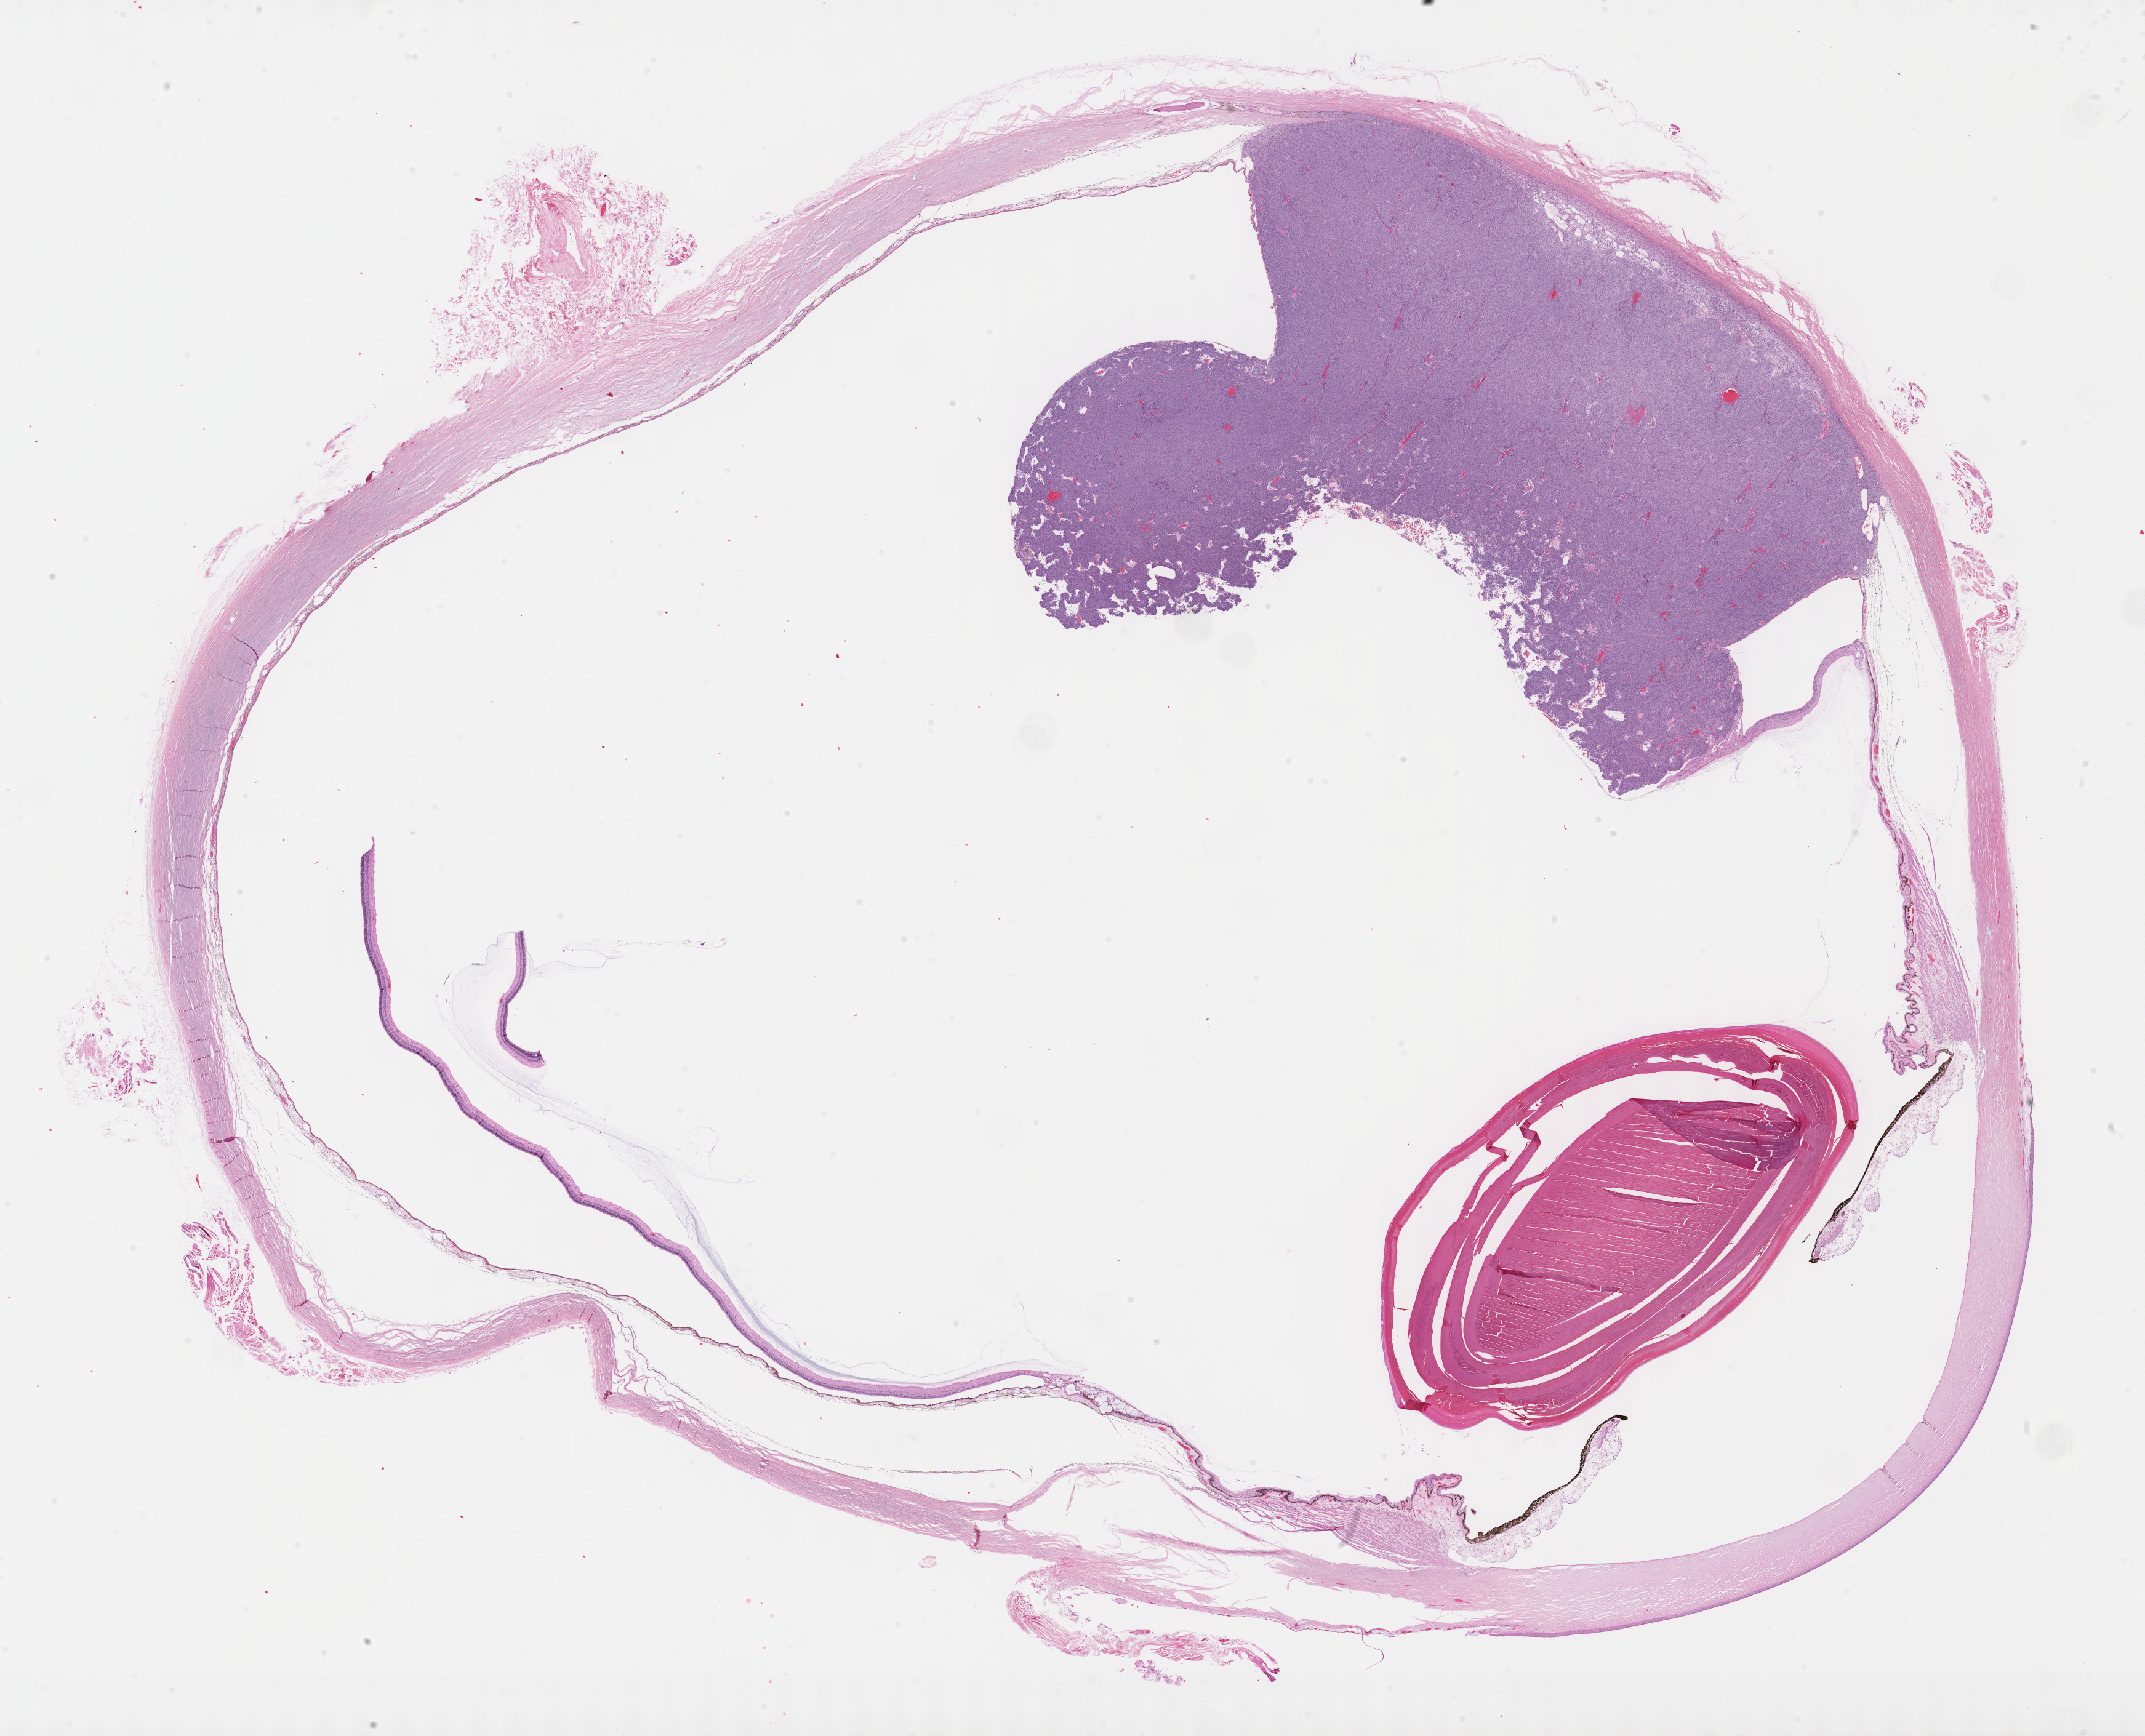
Digitized H&E tissue section (whole slide) — whole scanned area (about 28.2 x 22.8 mm, acquisition: 40x scan) shown as a low-resolution overview. Formalin-fixed paraffin-embedded (FFPE) diagnostic section. Primary tumour sample from the uvea. Male, age 64 years at initial diagnosis.
- diagnosis: Spindle cell melanoma, type B (choroid)
- AJCC pathologic stage: IIB (7th edition)